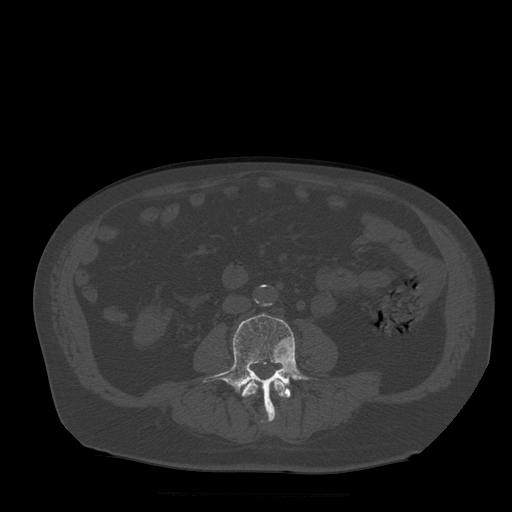
CT including the spine, one axial slice; bone window (W 1800 / L 400 HU); 1.25 mm slice thickness; 512 × 512 image matrix, field of view 420 × 420 mm. Patient age 72 years. Case-level facts recorded for this patient, not image findings: primary cancer: prostate.
Annotated regions visible in this slice (semi-automatic segmentation, software-assisted and operator-edited):
- L3 vertebra: bounding box <242,378,291,423> (left, top, right, bottom; pixels)
- L4 vertebra: <203,314,318,422>